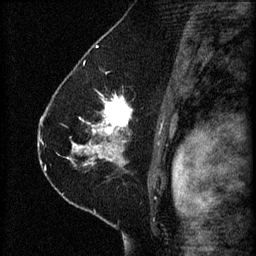
Breast MRI (dynamic contrast-enhanced), one sagittal slice. Slice 40 of 60 in the series (ordered by position). 3 images stored at this slice position (order not interpretable as contrast timing). 1.5 T. TE 4.2 ms, TR 8.2 ms. 2 mm slice thickness. 256 × 256 image matrix, field of view 180 × 180 mm. Patient: female, 41 years.
Annotated regions visible in this slice (semi-automatic segmentation, software-assisted and operator-edited):
- analysis volume of interest (the breast-tissue region the enhancement analysis was run in; not a lesion): bounding box (x1, y1, x2, y2) in pixels: (67, 92, 165, 173)
- tumour enhancement mask (voxels above the 70 % enhancement threshold inside the analysis volume of interest): (74, 94, 131, 165)